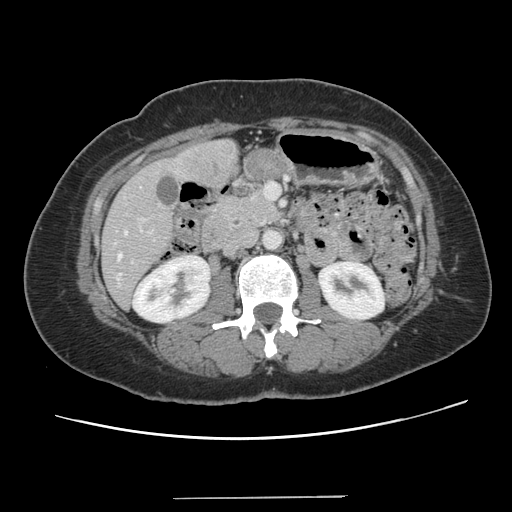
Contrast-enhanced abdominal CT, one axial slice; soft-tissue window (W 400 / L 40 HU); 512 × 512 image matrix, field of view 366 × 366 mm. Female patient, age 53 years. From the clinical record (not read from this slice): diagnosis: colorectal cancer liver metastases, imaged before liver resection; multiple liver metastases: no; largest metastasis: 14.5 cm.
Outlined on this slice (manually delineated by an expert):
- hepatic veins: box from (x=117, y=231) to (x=127, y=260) px
- liver: (x=102, y=141)–(x=237, y=307)
- planned liver remnant (the part of the liver to remain after resection): (x=101, y=218)–(x=173, y=307)